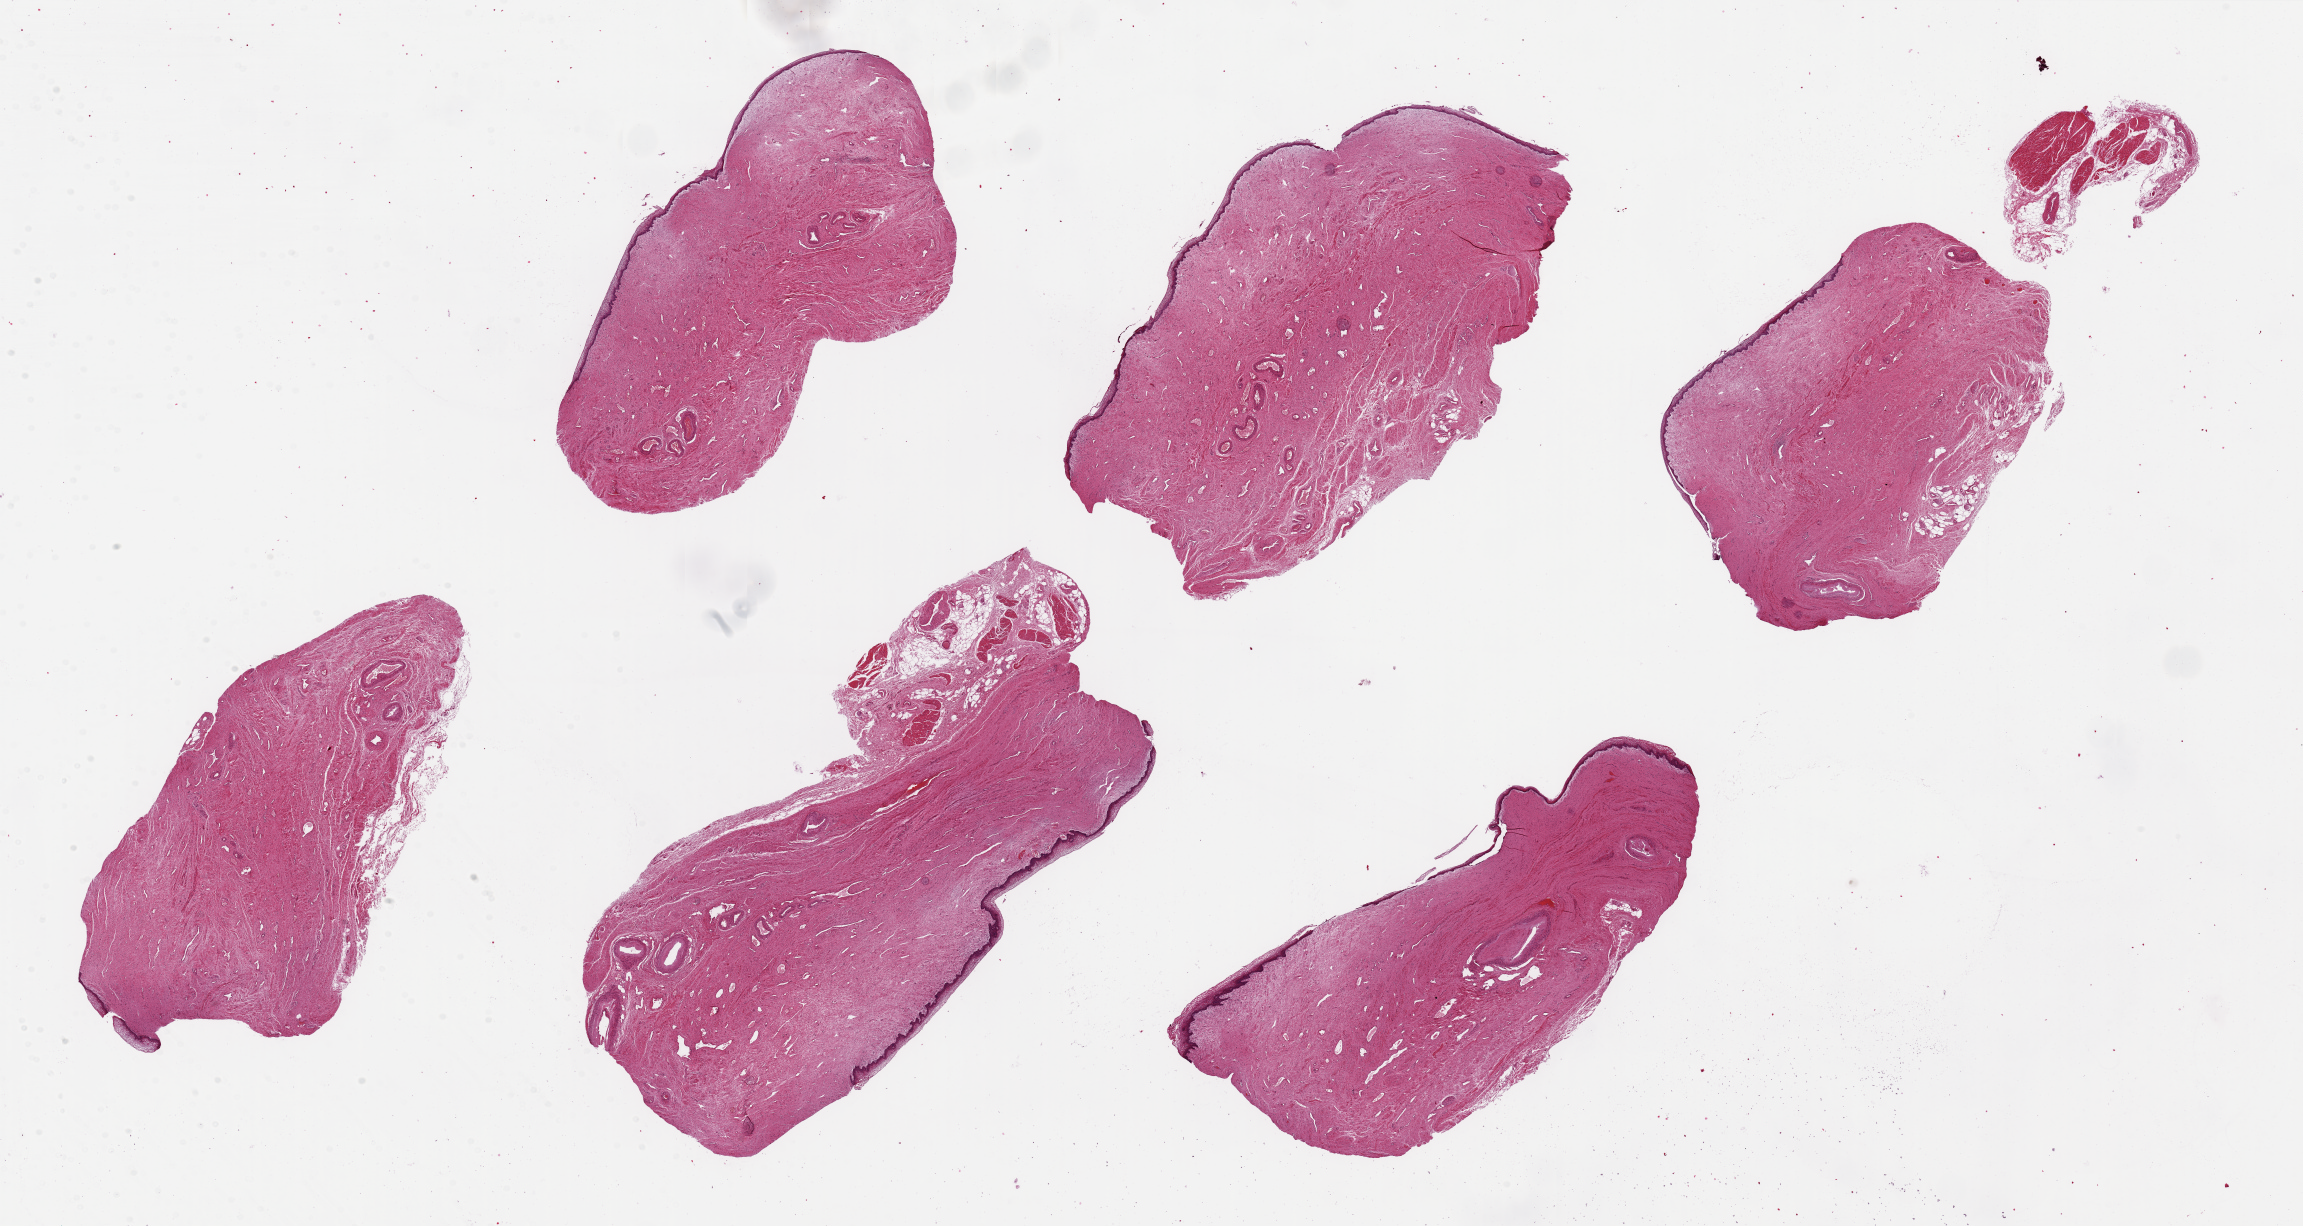
Digitized hematoxylin and eosin (H&E)-stained section, brightfield, whole scanned area (about 36.4 x 19.4 mm) shown as a low-resolution overview, PAXgene-fixed paraffin-embedded (PFPE) section, section of vagina (target tissue), tissue donor sample.
Reviewer comment on this tissue sample: 6 pieces ~8x4mm. Squamous mucosa, partly detached, <2% thickness. Minimal attached fat.